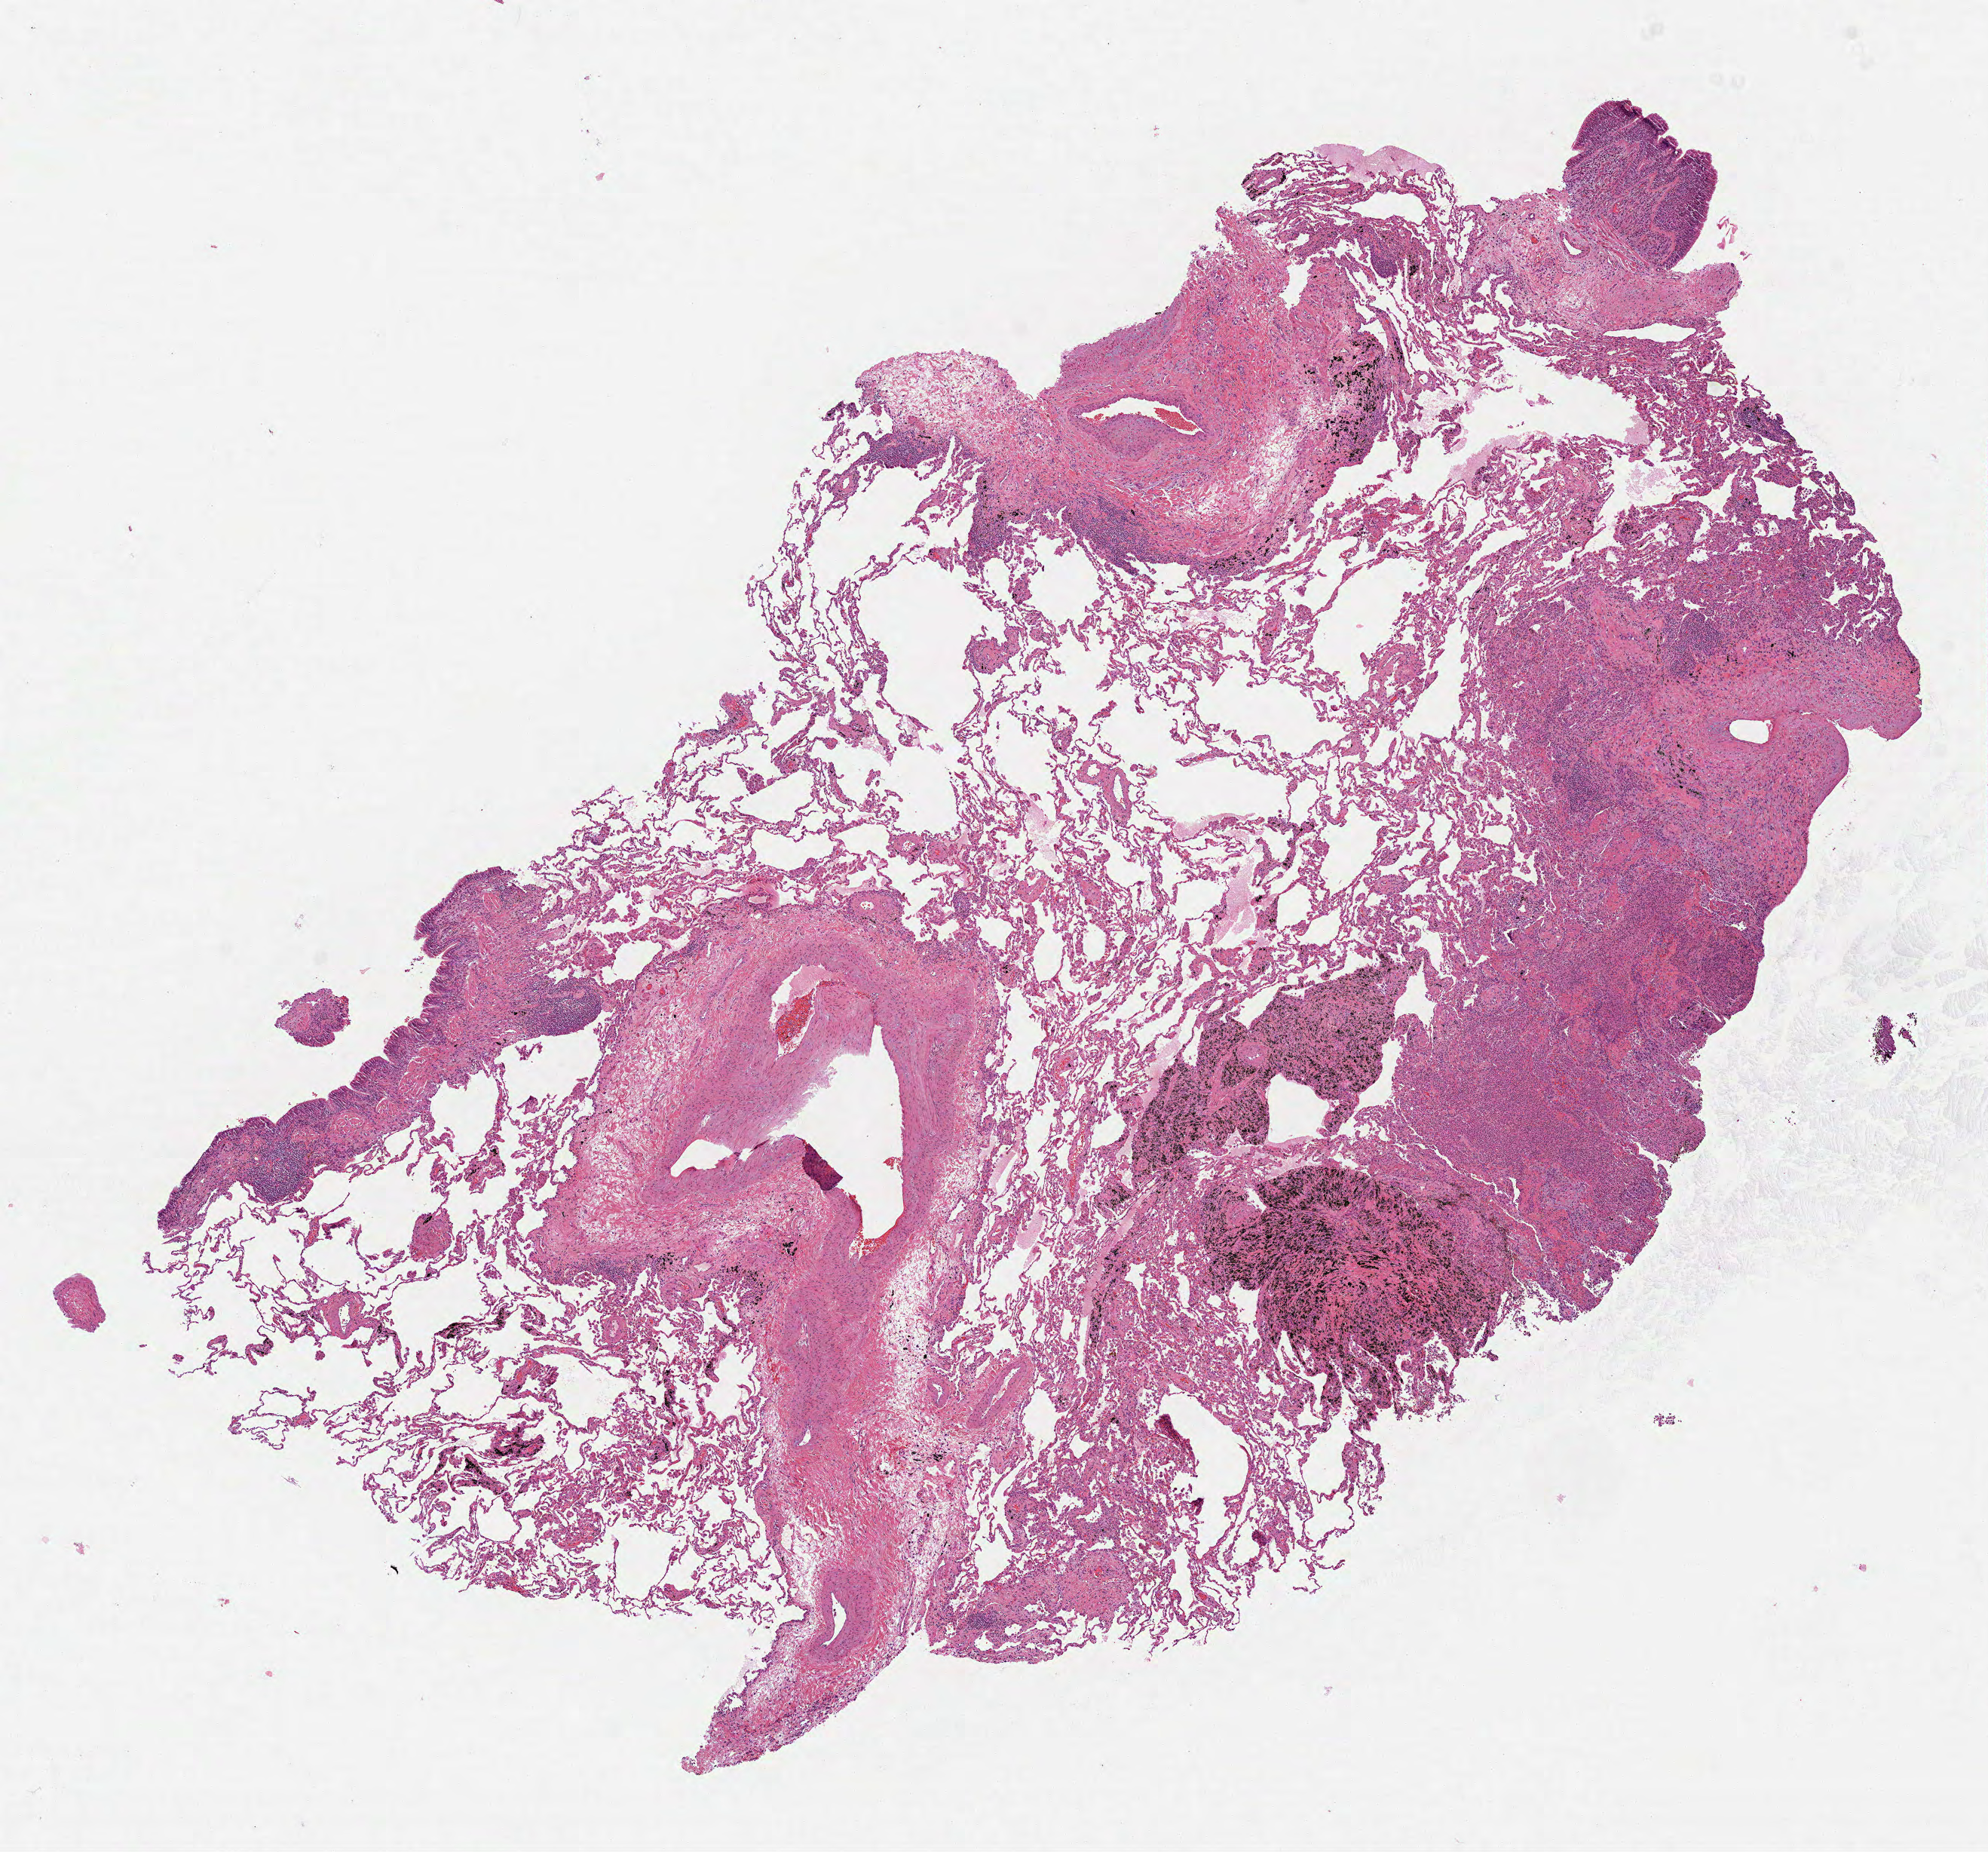
Digitized H&E tissue section (whole slide) — shown as a low-resolution overview of the whole scanned area (about 10.6 x 9.9 mm); formalin-fixed paraffin-embedded (FFPE) diagnostic section; primary tumour sample from the lung. Male patient; age at initial diagnosis 84 years.
Diagnosis: Squamous cell carcinoma, NOS (lower lobe, lung). AJCC pathologic stage: IB.